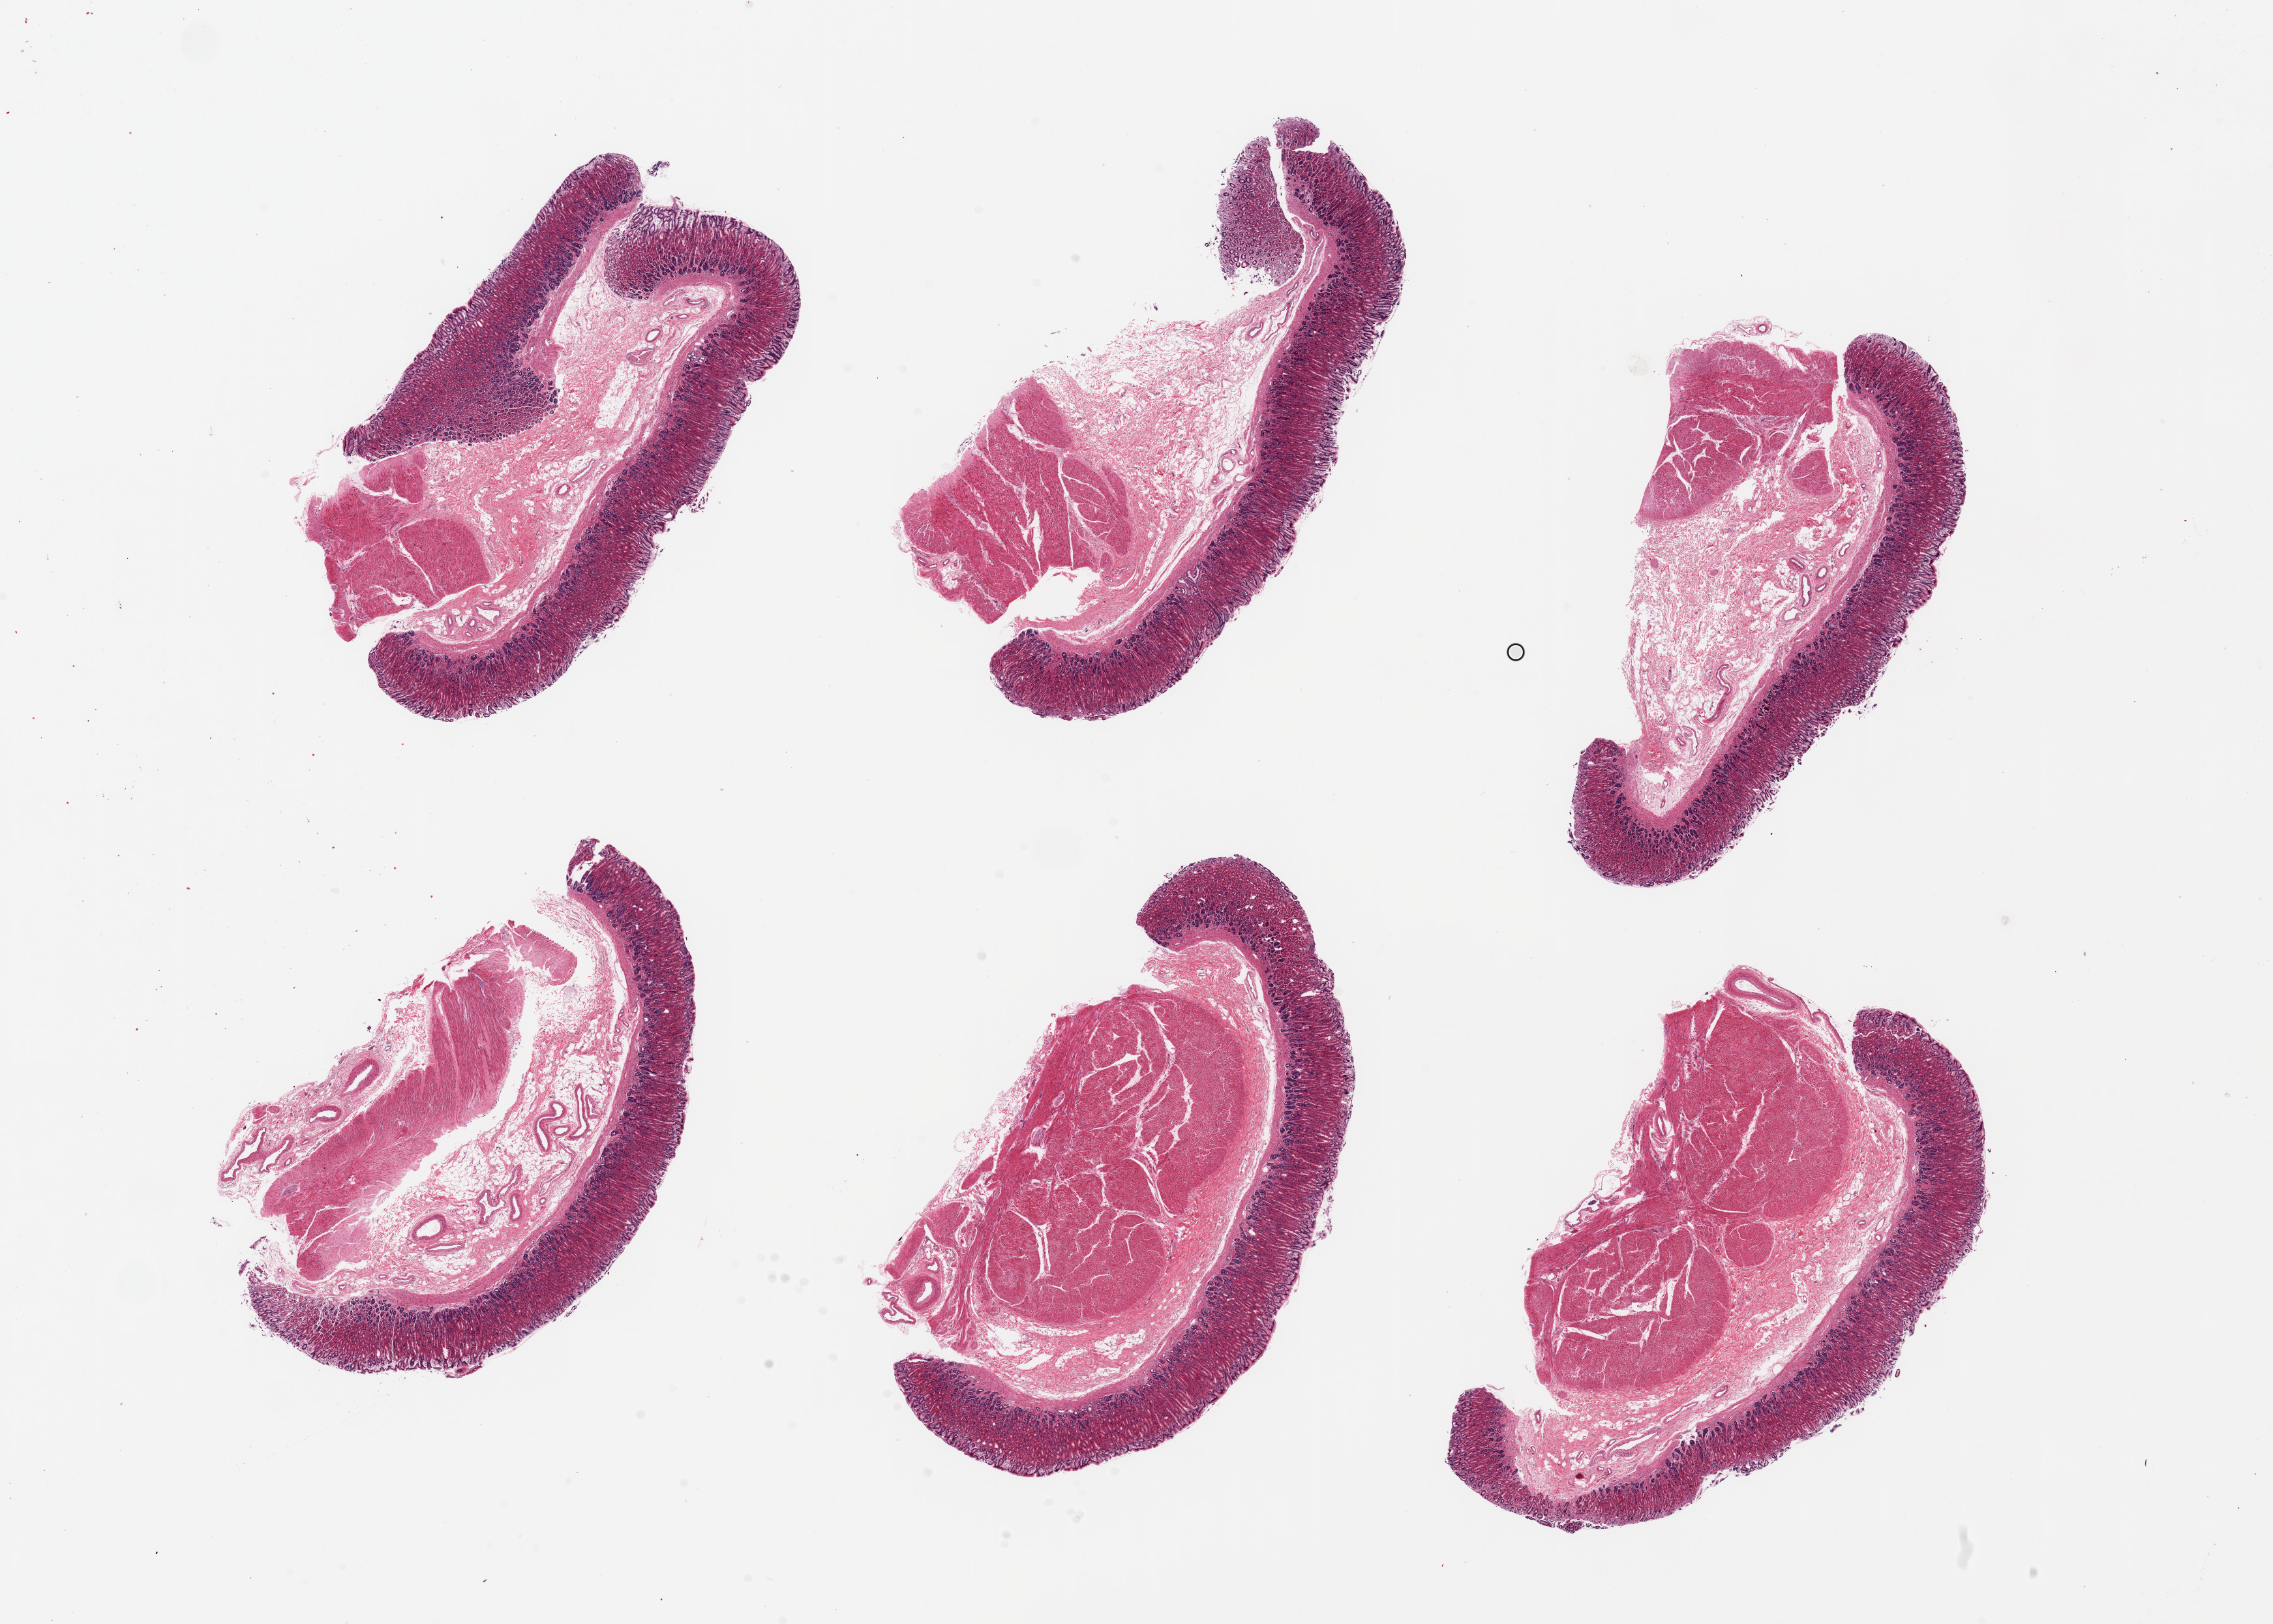
Whole-slide image, hematoxylin and eosin (H&E) stain, brightfield, whole scanned area (about 27.6 x 19.7 mm) shown as a low-resolution overview. PAXgene-fixed paraffin-embedded (PFPE) section. Section of stomach (target tissue). Donor tissue sample.
• reviewer comment on this tissue sample: 6 pieces ~7x4mm, ~20% mucosa, well preserved